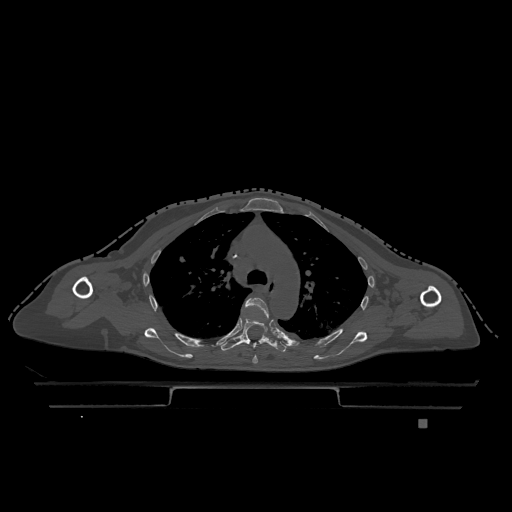
CT including the spine, one axial slice; slice 853 of 1317 in the series (ordered by position); bone window (W 1800 / L 400 HU); 0.5 mm slice thickness; 512 × 512 image matrix. Female patient, age 74 years. From the clinical record (not read from this slice): primary cancer: lung; vertebrae with lytic lesions (as recorded): T1, T4, T5, T6, L4, L5.
Annotated regions visible in this slice (semi-automatic segmentation, software-assisted and operator-edited):
- T4 vertebra: bounding box (x1, y1, x2, y2) in pixels: (245, 297, 269, 364)
- T5 vertebra: (220, 316, 288, 353)